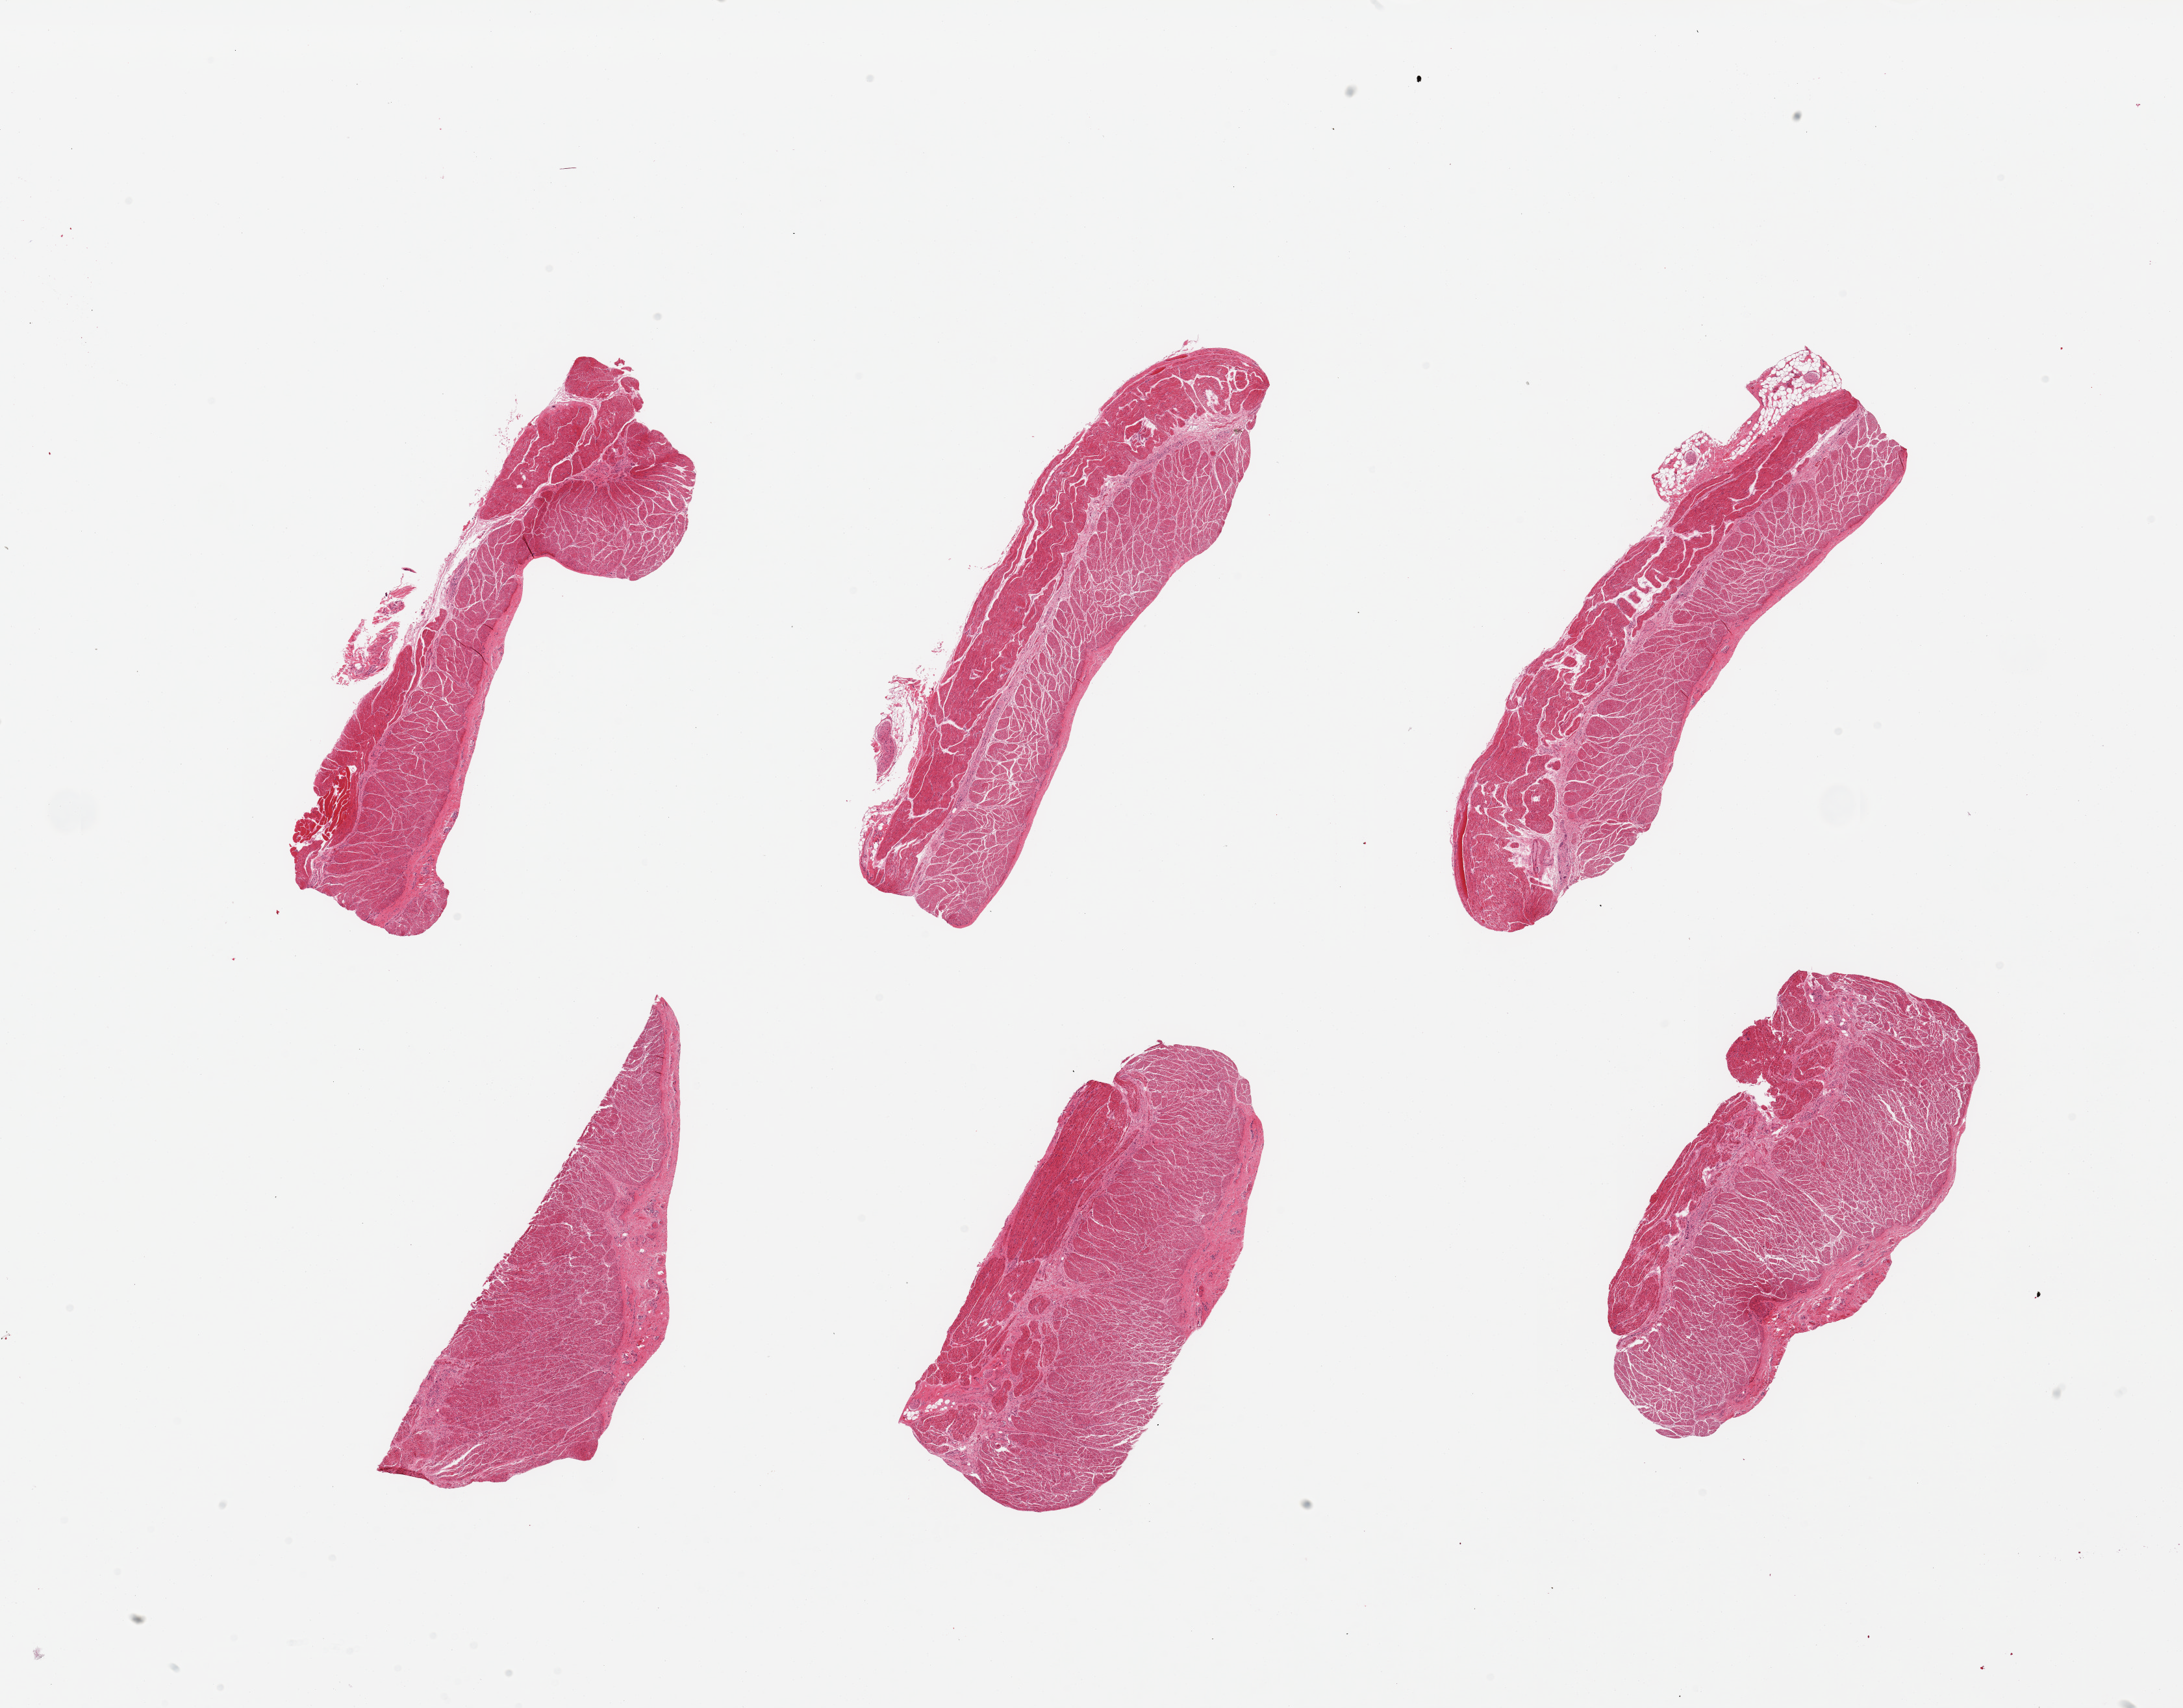
Whole-slide image, haematoxylin and eosin stain — whole scanned area (about 26.6 x 20.8 mm, acquisition: 20x scan) shown as a low-resolution overview; PAXgene-fixed paraffin-embedded (PFPE) section; section of esophageal muscle (target tissue); donor tissue sample. Male donor.
- reviewer comment on this tissue sample: 6 pieces; well dissected